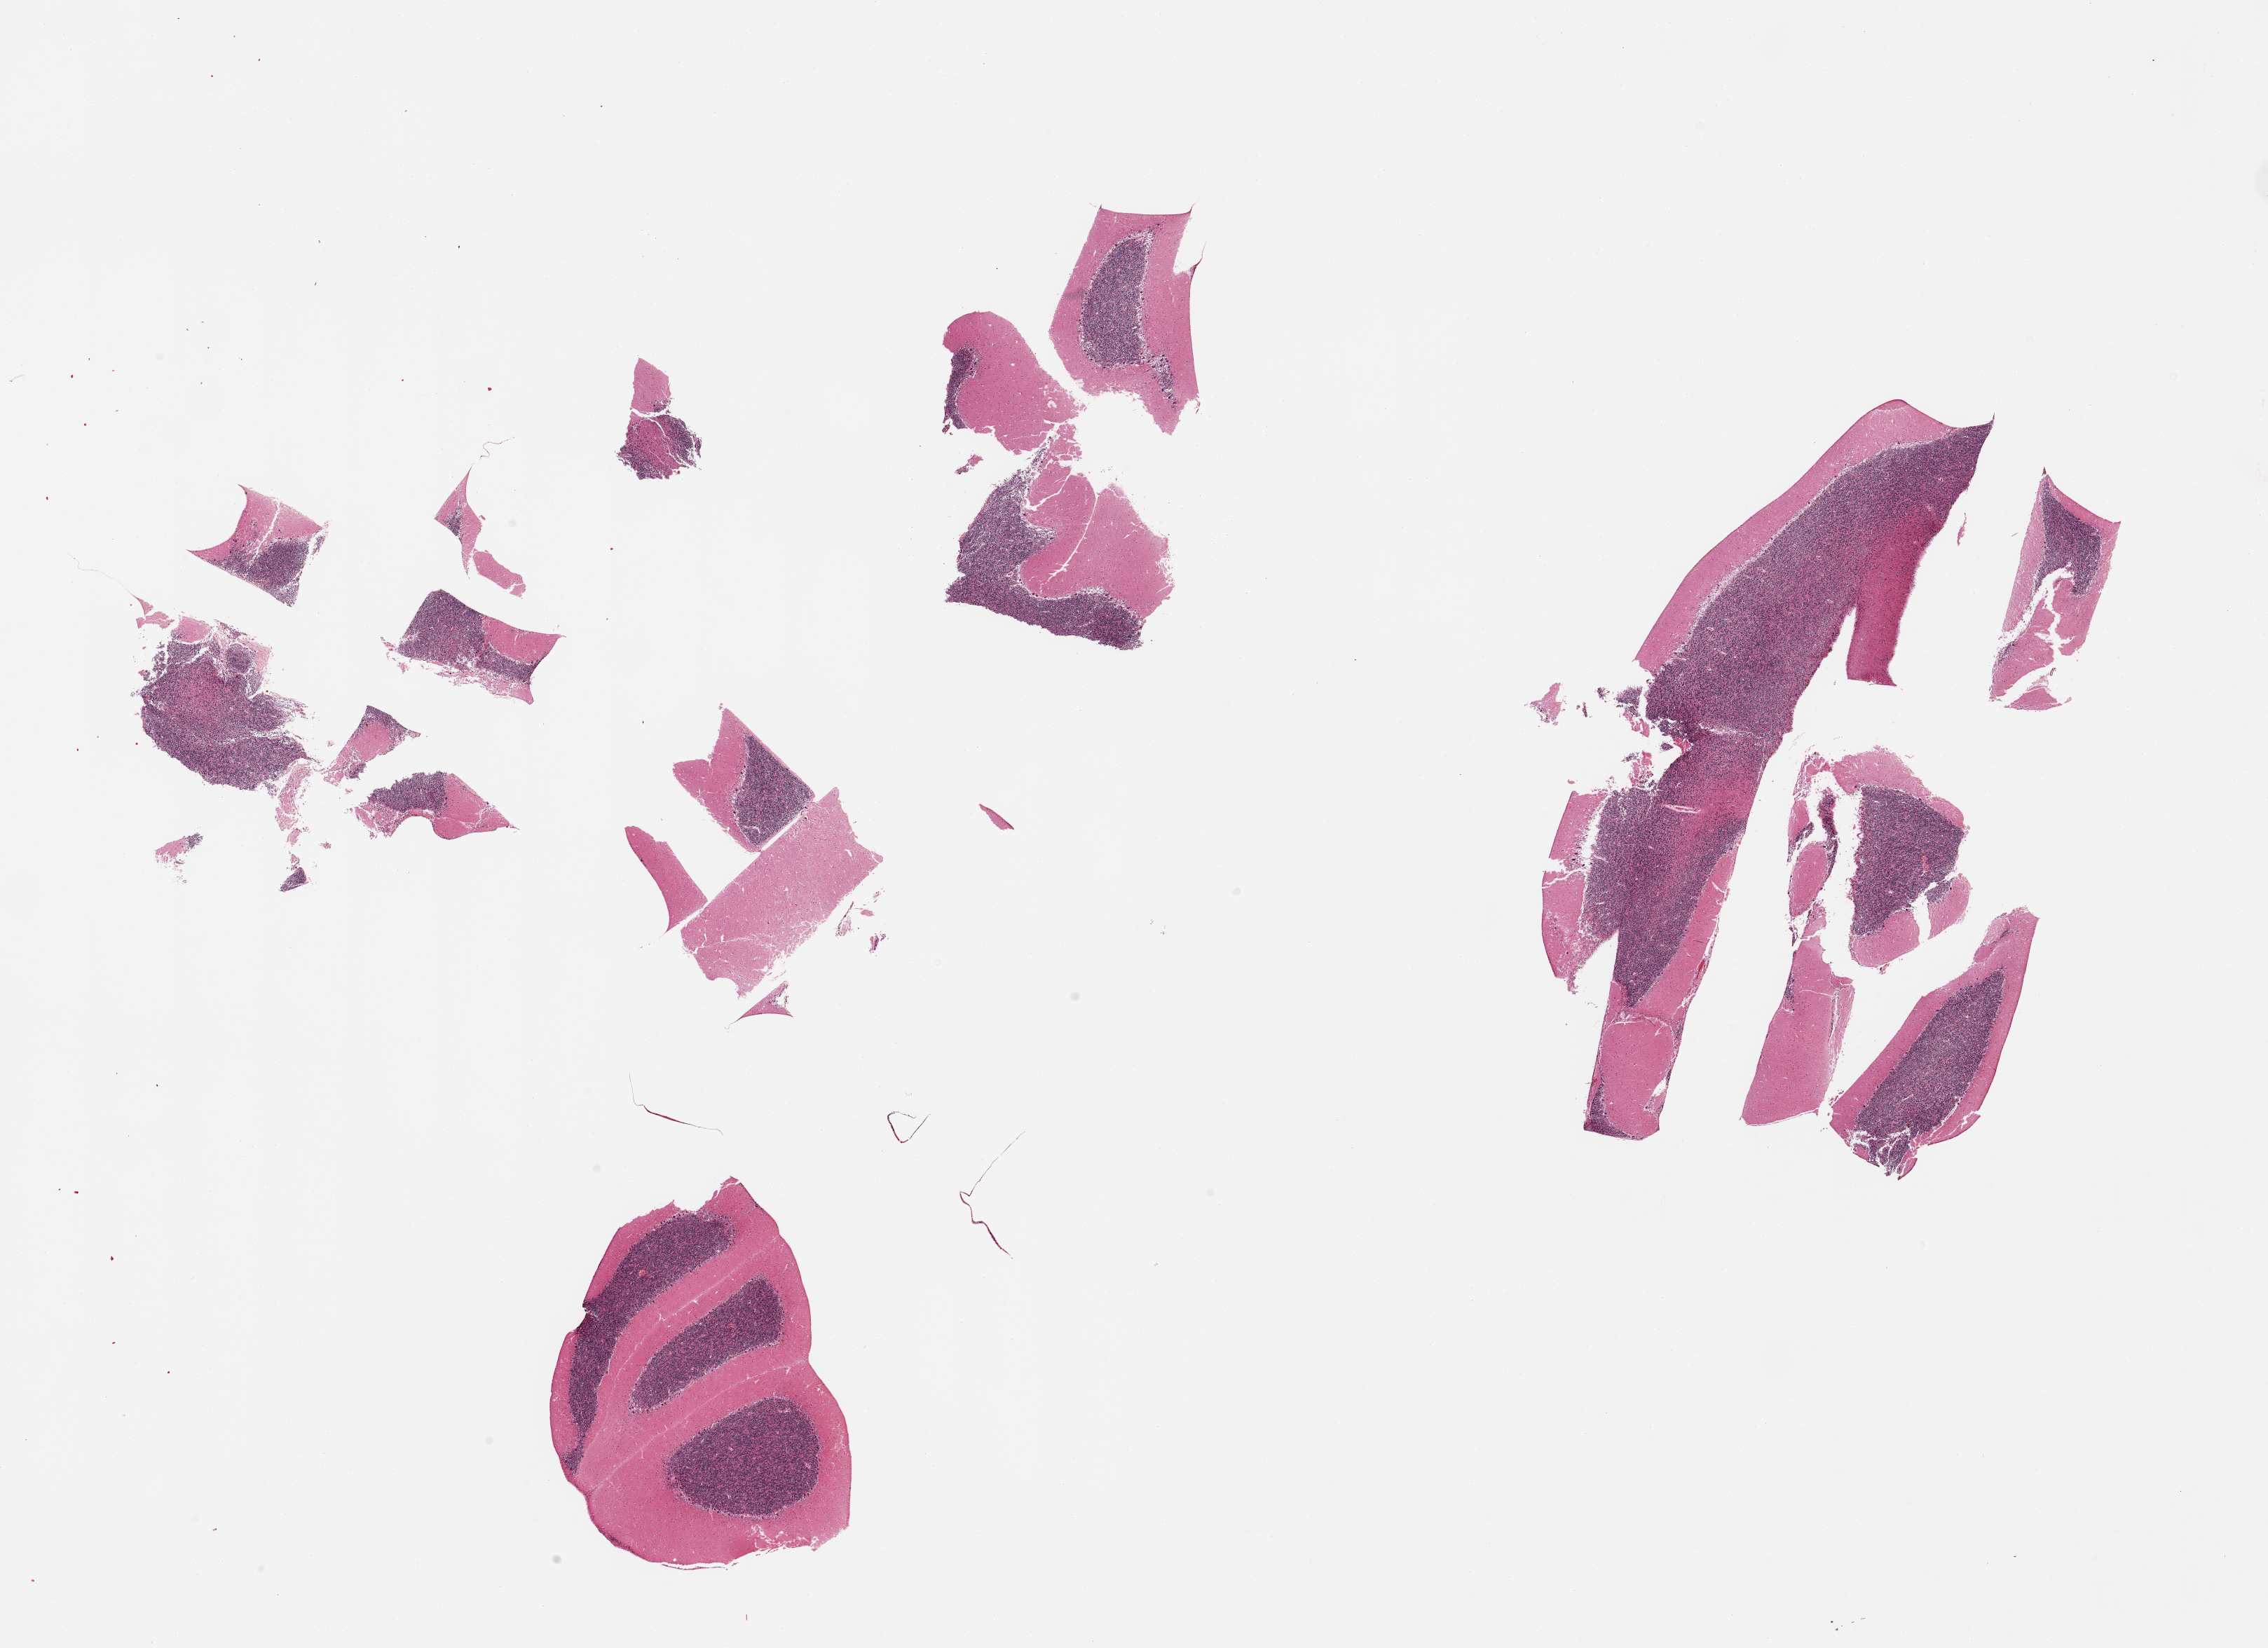
Hematoxylin and eosin (H&E) whole-slide image, a low-resolution overview of the entire scanned area, about 25.6 x 18.6 mm. PAXgene-fixed paraffin-embedded (PFPE) section. Section of cerebellum (target tissue). Donor tissue sample.
Review note (as recorded): 2 pieces; two pieces markedly fragmented.